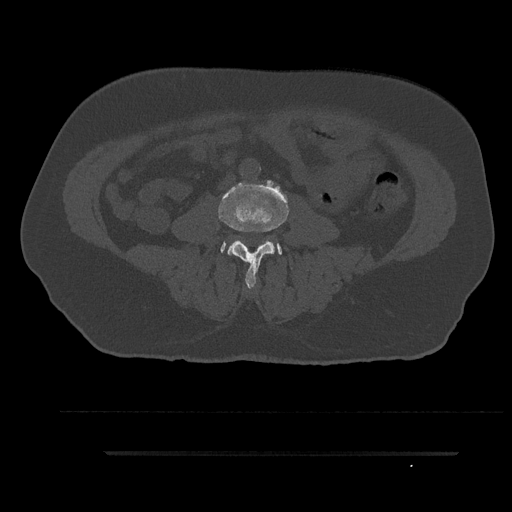
CT including the spine, one axial slice; position 18 of 797 along the scan axis; reconstruction kernel Br40s/3; bone window (W 1800 / L 400 HU); 0.5 mm slice thickness; 512 × 512 image matrix, field of view 432 × 432 mm. Patient: male, 63 years. Case-level facts recorded for this patient, not image findings: primary cancer: renal; vertebrae with lytic lesions (as recorded): T8.
Outlined on this slice (semi-automatically segmented with operator editing):
- L3 vertebra: bounding box (x1, y1, x2, y2) in pixels: (219, 185, 289, 290)
- L4 vertebra: (221, 241, 282, 255)